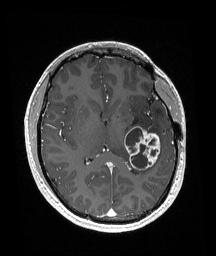
Brain MRI from a brain-tumour surgery series, one axial slice; slice 89 of 192 in the series (ordered by position); T1-weighted post-contrast; 216 × 256 image matrix, field of view 211 × 250 mm. From the clinical record (not read from this slice): histopathology: Glioneuronal tumor; WHO grade: 2.
Structures marked on this image (expert manual segmentation):
- tumour: bounding box (x1, y1, x2, y2) in pixels: (124, 126, 161, 171)